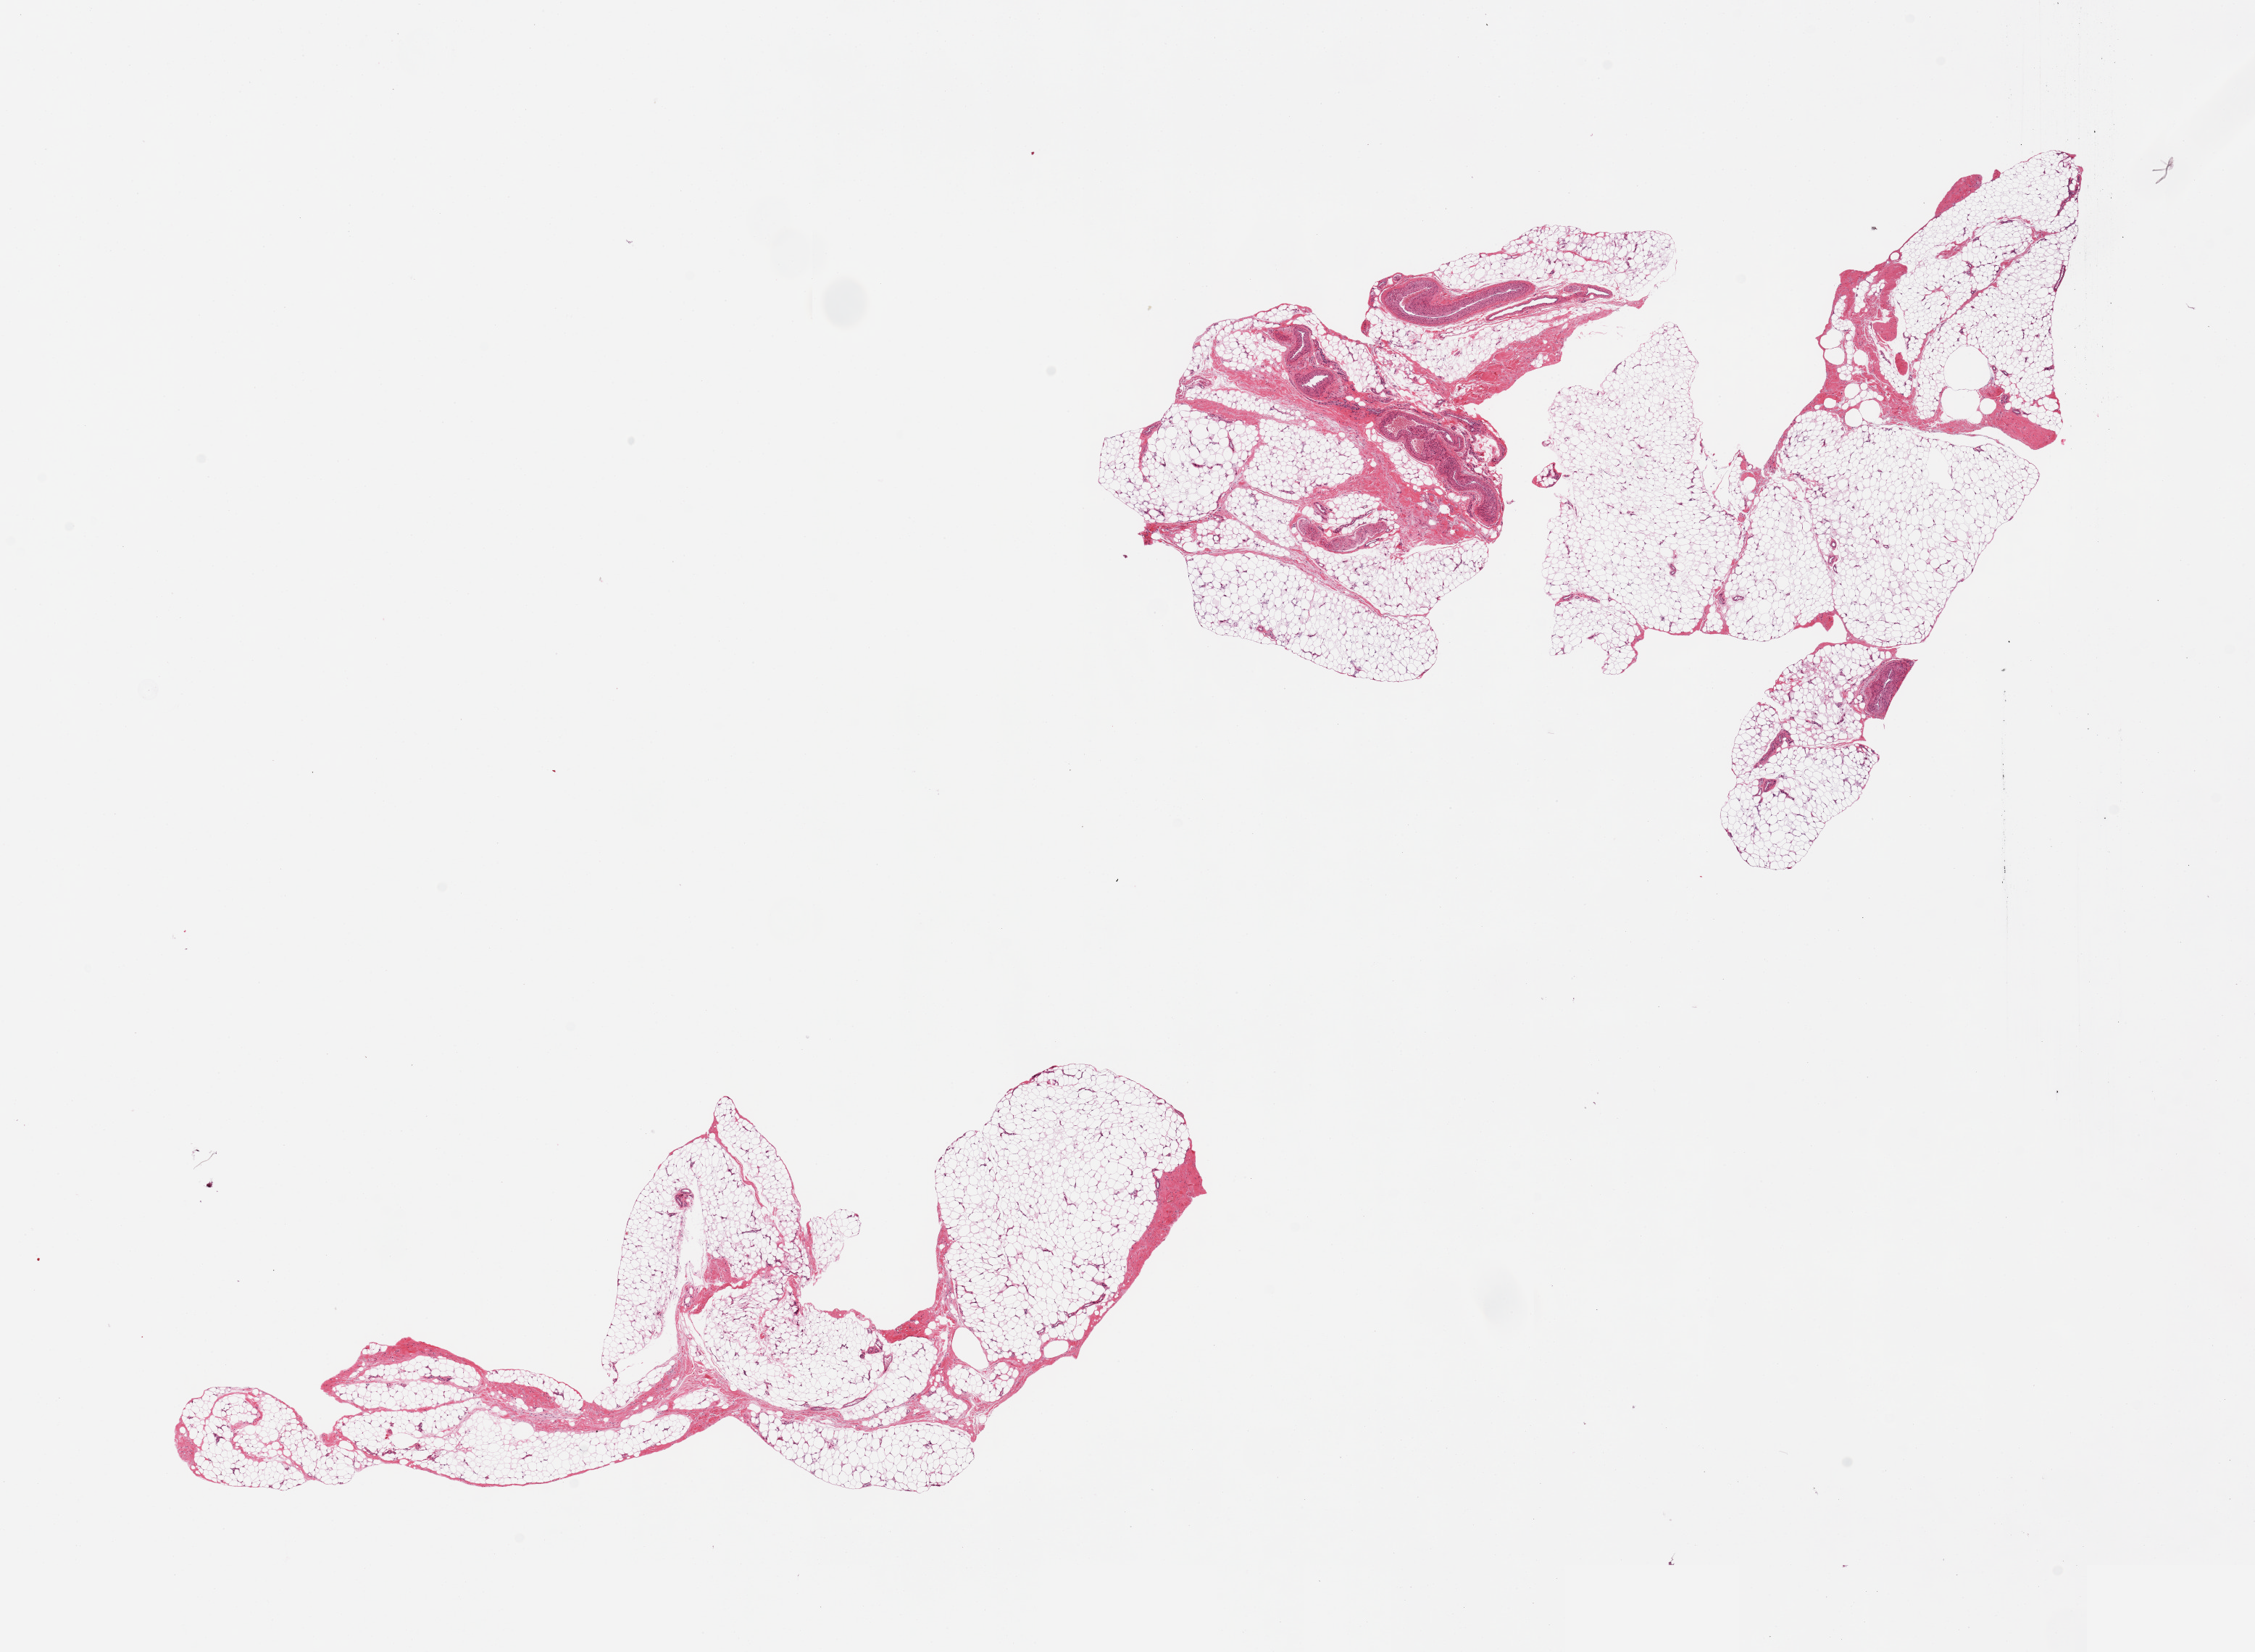
Whole-slide image, haematoxylin and eosin stain, low-resolution overview of the scanned area, about 24.6 x 18.0 mm (from a 20x scan); PAXgene-fixed, paraffin-embedded tissue; target tissue: adipose tissue; donor tissue sample. Donor sex: male.
Reviewer comment on this tissue sample: 2 pieces, ~10% fibrovacular tissue; dlineated.